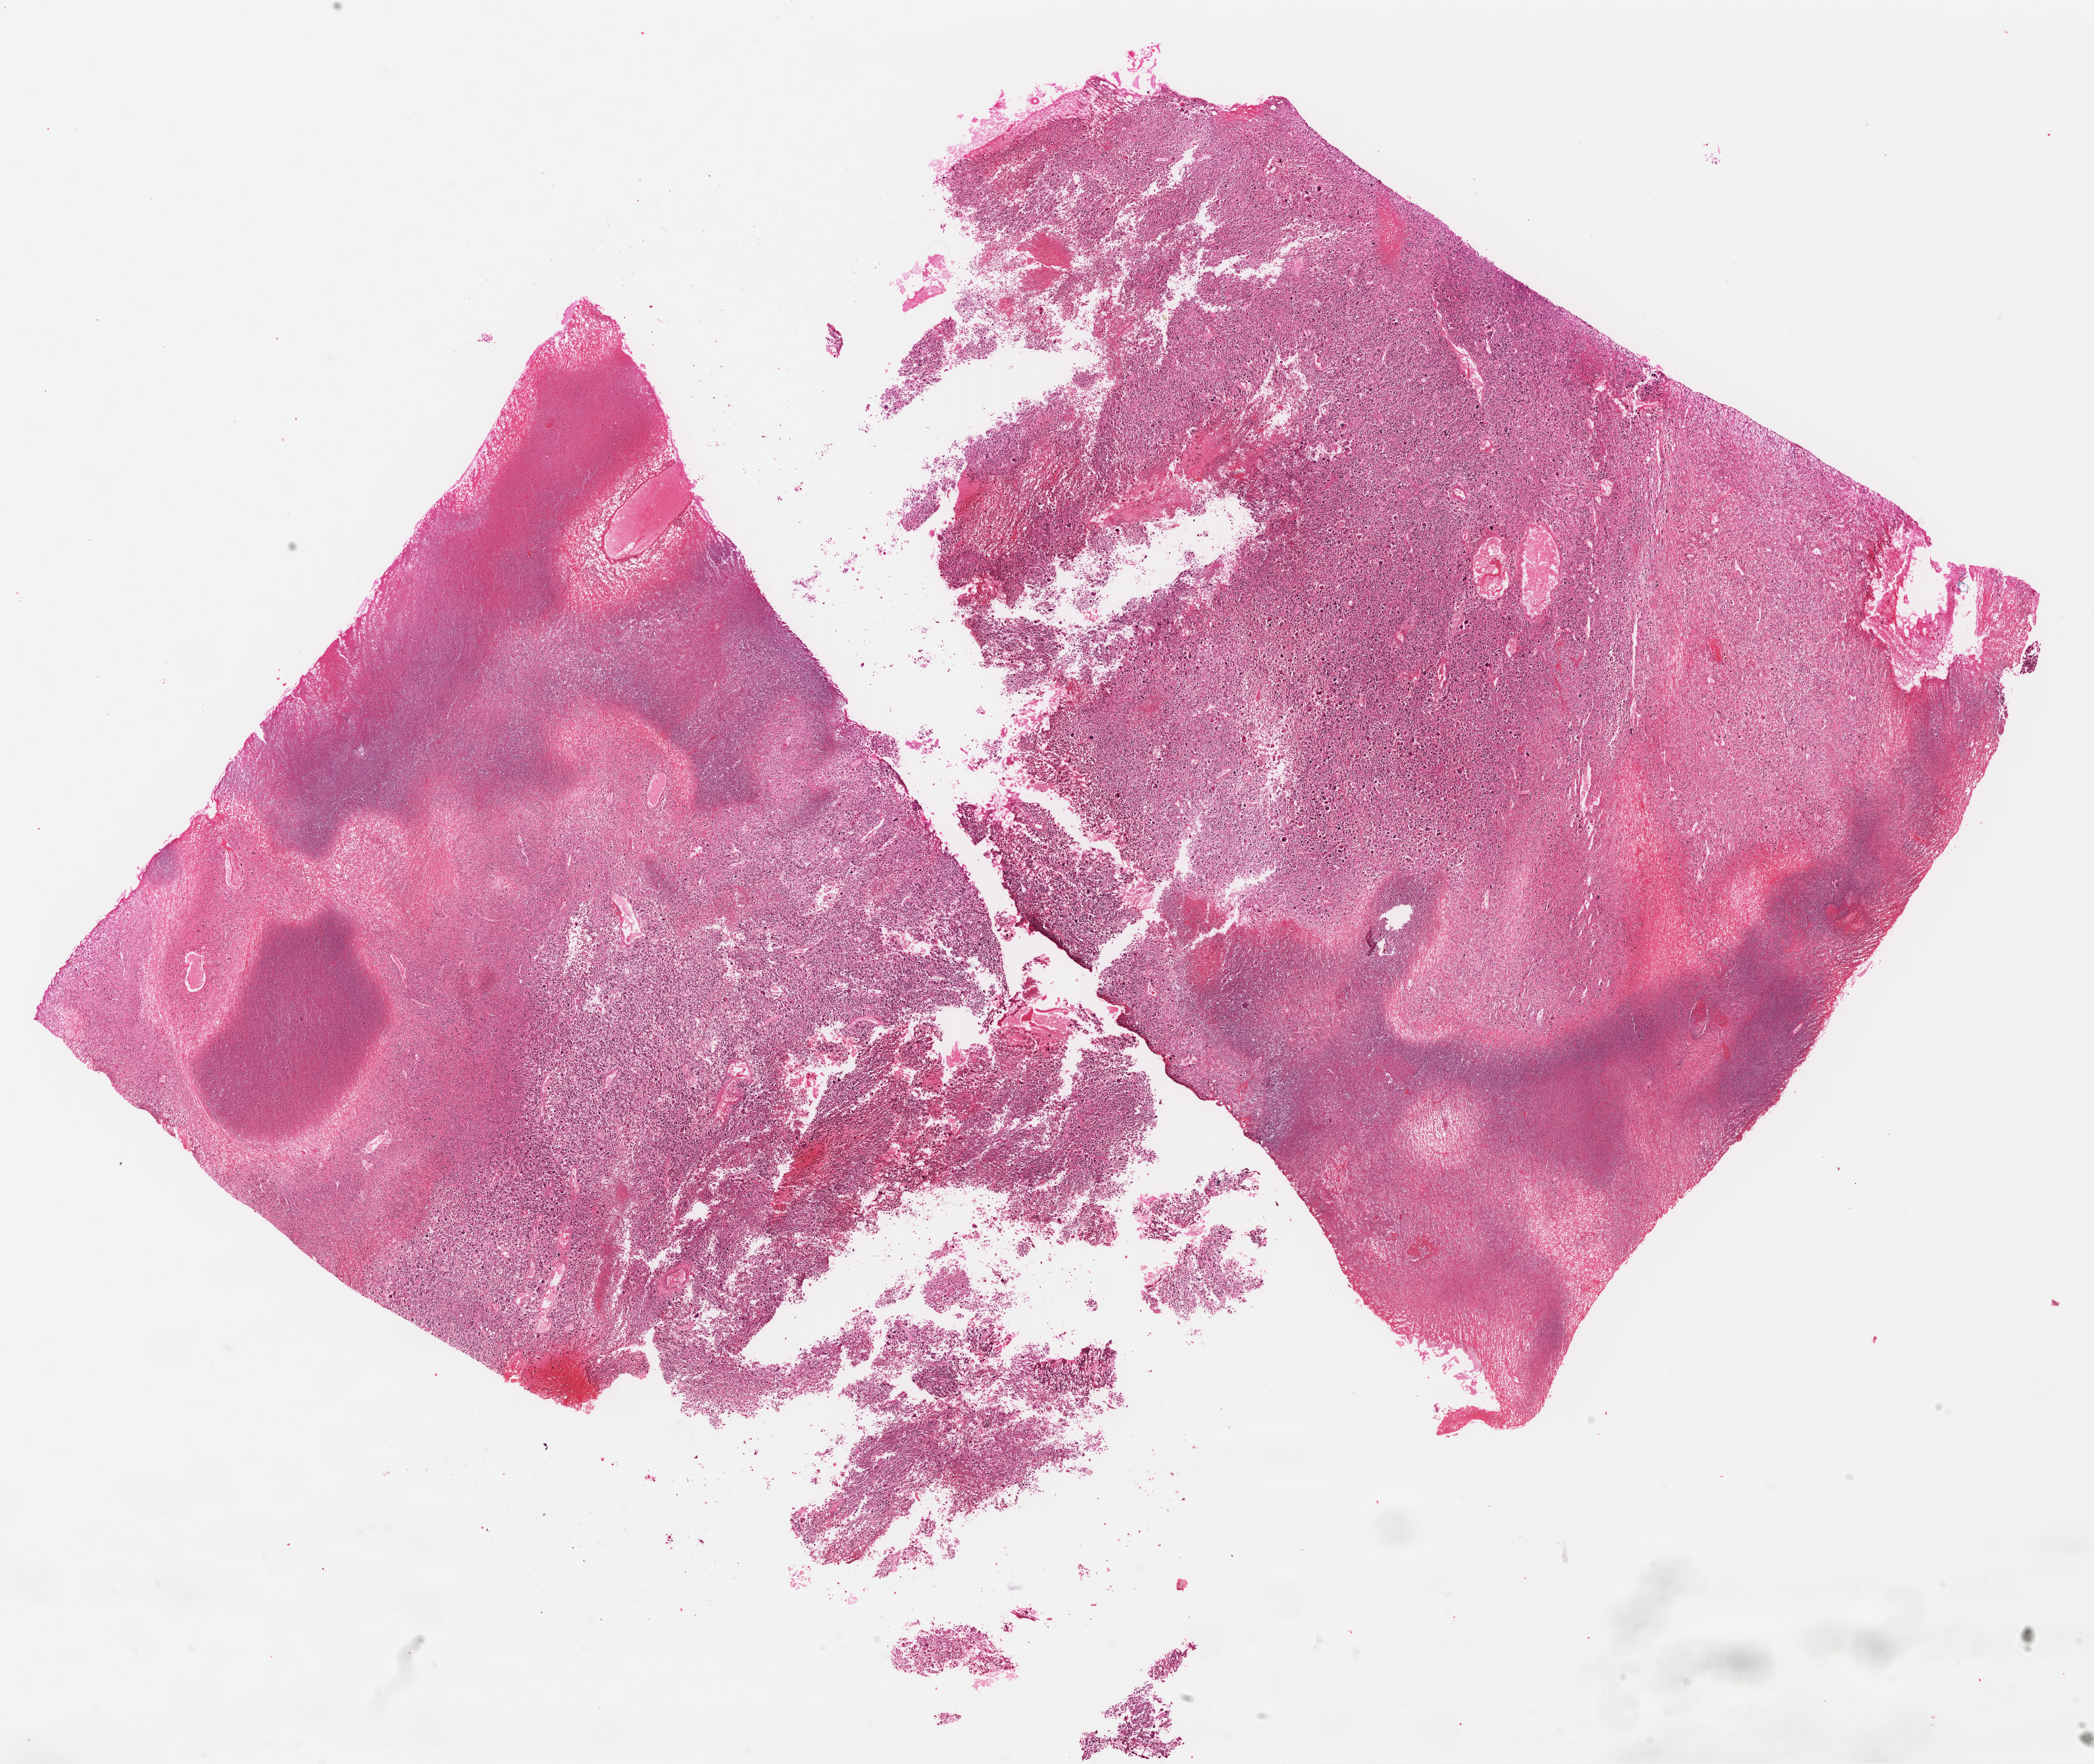
Whole-slide histology image, H&E — whole scanned area (about 25.0 x 21.1 mm) shown as a low-resolution overview. Formalin-fixed paraffin-embedded (FFPE) diagnostic section. Connective, subcutaneous and other soft tissues, primary tumour sample. Patient: male, age at initial diagnosis 73 years.
Diagnosis: Leiomyosarcoma, NOS (connective, subcutaneous and other soft tissues, NOS).